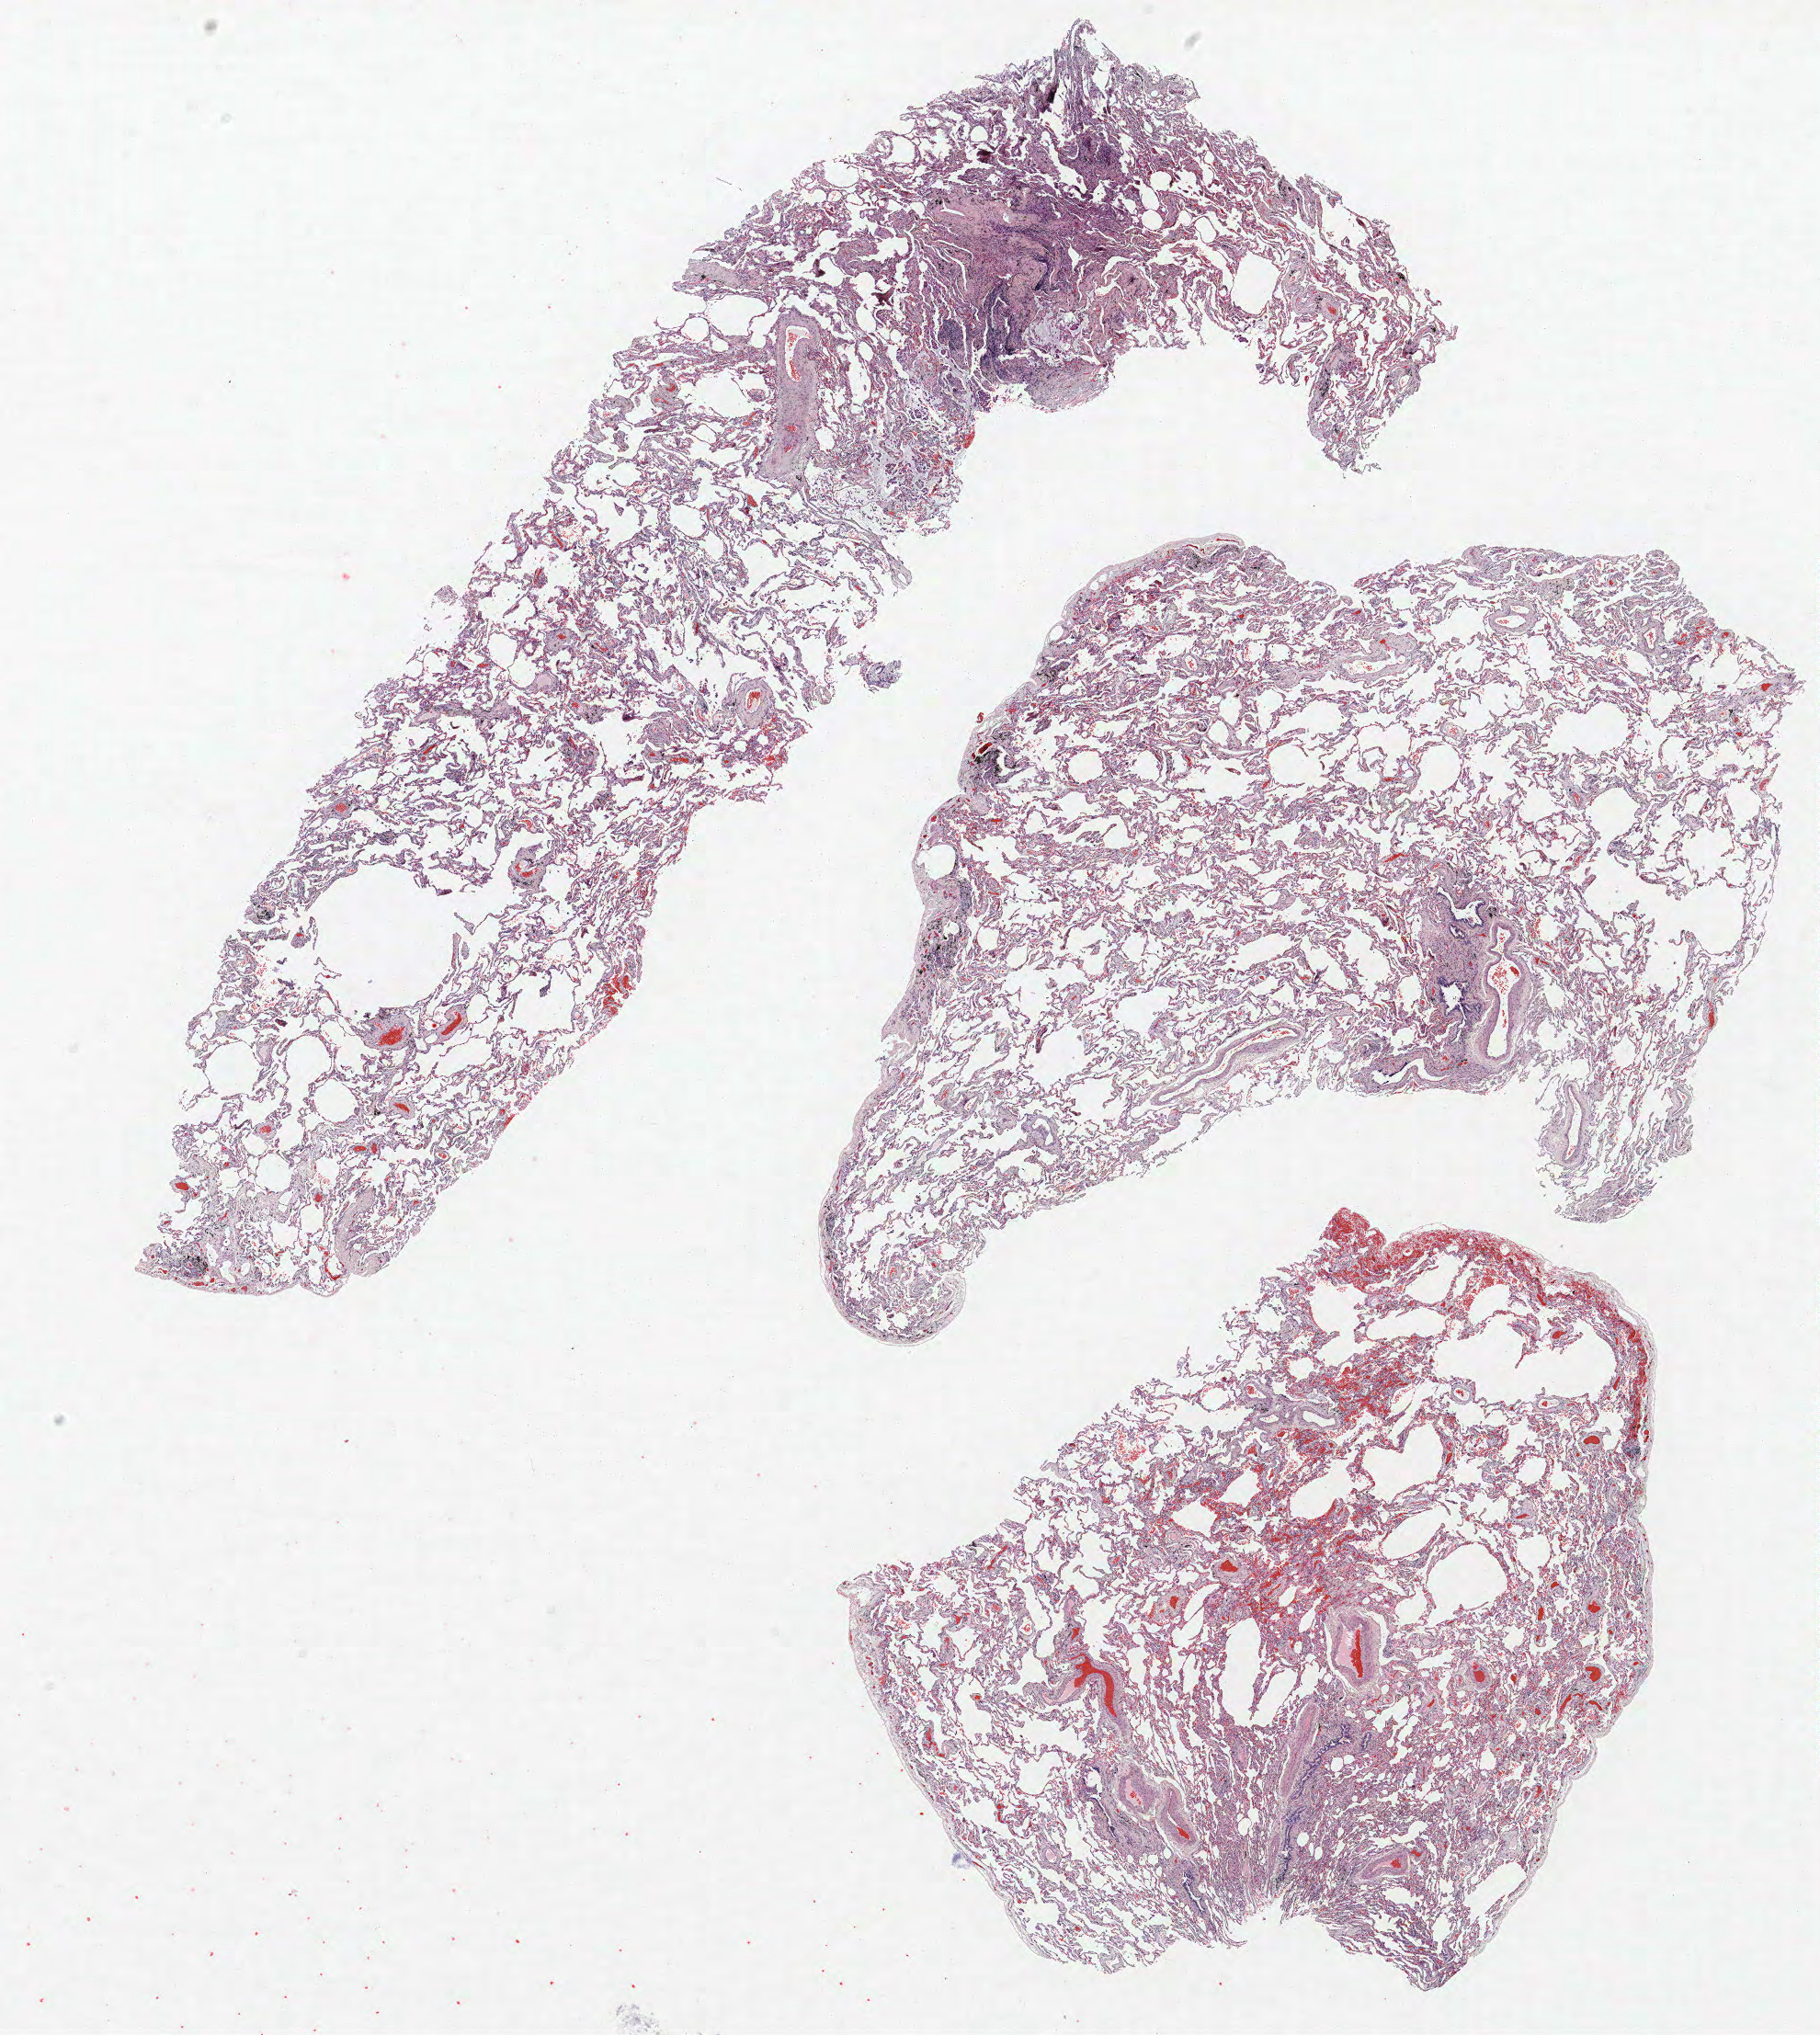
Whole-slide histology image, H&E-stained, shown as a low-resolution overview of the whole scanned area (about 15.8 x 17.7 mm, acquisition: 40x scan). Formalin-fixed paraffin-embedded (FFPE) section. Lung tissue. Female, age 68 at enrolment. Former smoker at enrolment. Grade: well differentiated (G1).
• stage (AJCC 6th edition): IV
• participant's lung-cancer diagnosis: Bronchiolo-alveolar adenocarcinoma, NOS (ICD-O-3 8250/3)
• primary tumour location (clinical record): right upper lobe, right middle lobe, right lower lobe